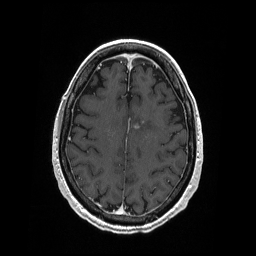
Brain MRI from a brain-tumour surgery series, one axial slice. Position 71 of 208 along the scan axis. T1-weighted post-contrast. 1 mm slice thickness. 256 × 256 image matrix. Case-level facts recorded for this patient, not image findings: histopathology: Primary diffuse large B-cell lymphoma.
Annotated regions visible in this slice (expert manual segmentation):
- tumour: bounding box (x1, y1, x2, y2) in pixels: (134, 121, 145, 129)